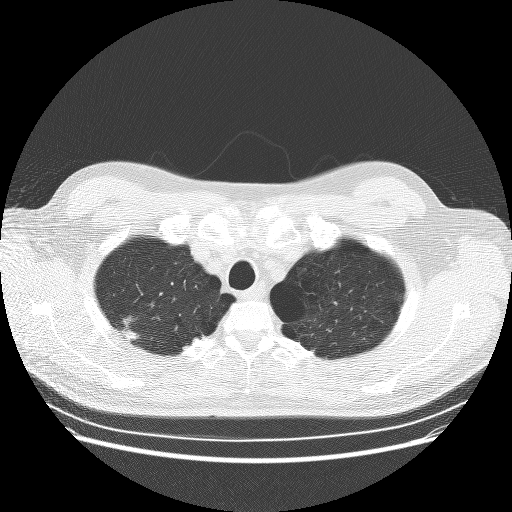
Low-dose screening chest CT, one axial slice; position 229 of 253 along the scan axis; reconstruction kernel BONE; 120 kVp; lung window (W 1500 / L -600 HU); 2.5 mm slice thickness; 512 × 512 image matrix.
Outlined on this slice (outlined manually by an expert reader):
- lesion 1 (tumor, upper lobe of right lung): bounding box [x1, y1, x2, y2] px = [122, 318, 139, 341]